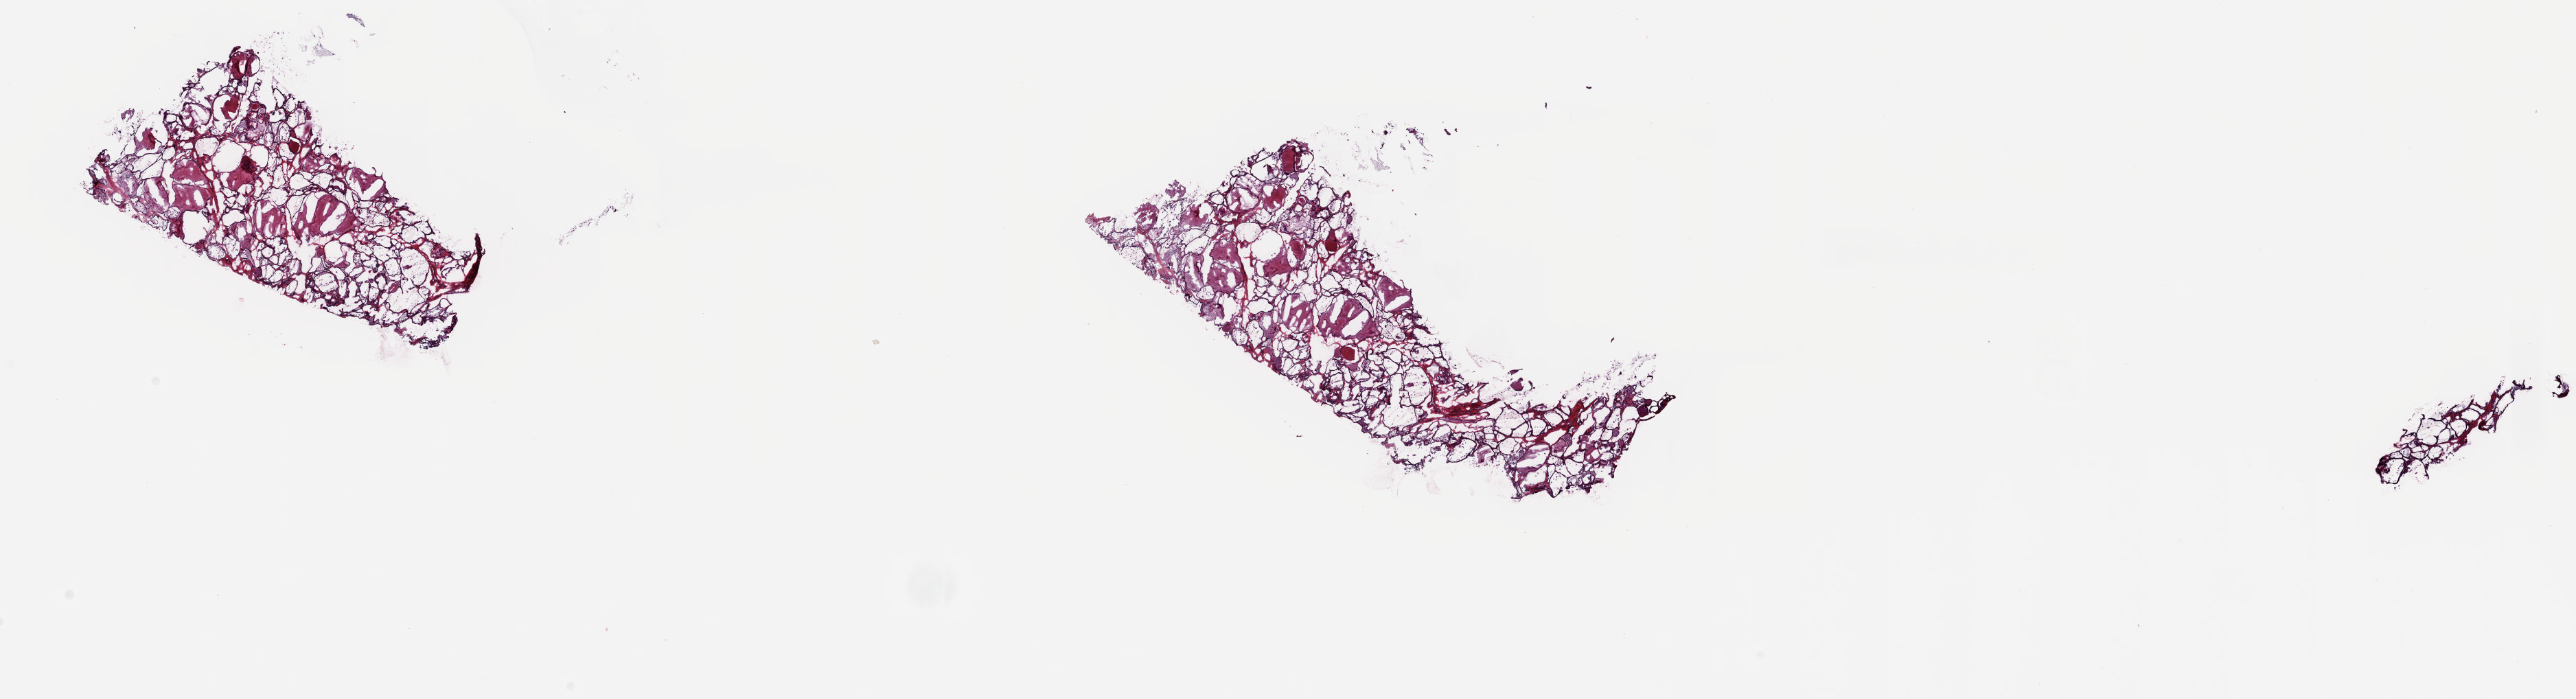
Digitized Hematoxylin and eosin (H&E) stained tissue section (whole slide) — whole scanned area (about 29.8 x 8.1 mm) shown as a low-resolution overview. Frozen section from the top of the tissue portion. Solid tissue normal (non-tumour tissue) sample from the thyroid. Female, age 37 years at initial diagnosis. Pathologist review of this section (percent, as recorded): tumour cells 0%, tumour nuclei 0%, normal cells 100%, stromal cells 0%, necrosis 0%. Inflammatory infiltration, as recorded: lymphocyte infiltration 0%, monocyte infiltration 1%, neutrophil infiltration 0%.
This section: solid tissue normal sample (biorepository sample class). Patient diagnosis: Papillary adenocarcinoma, NOS (thyroid gland).